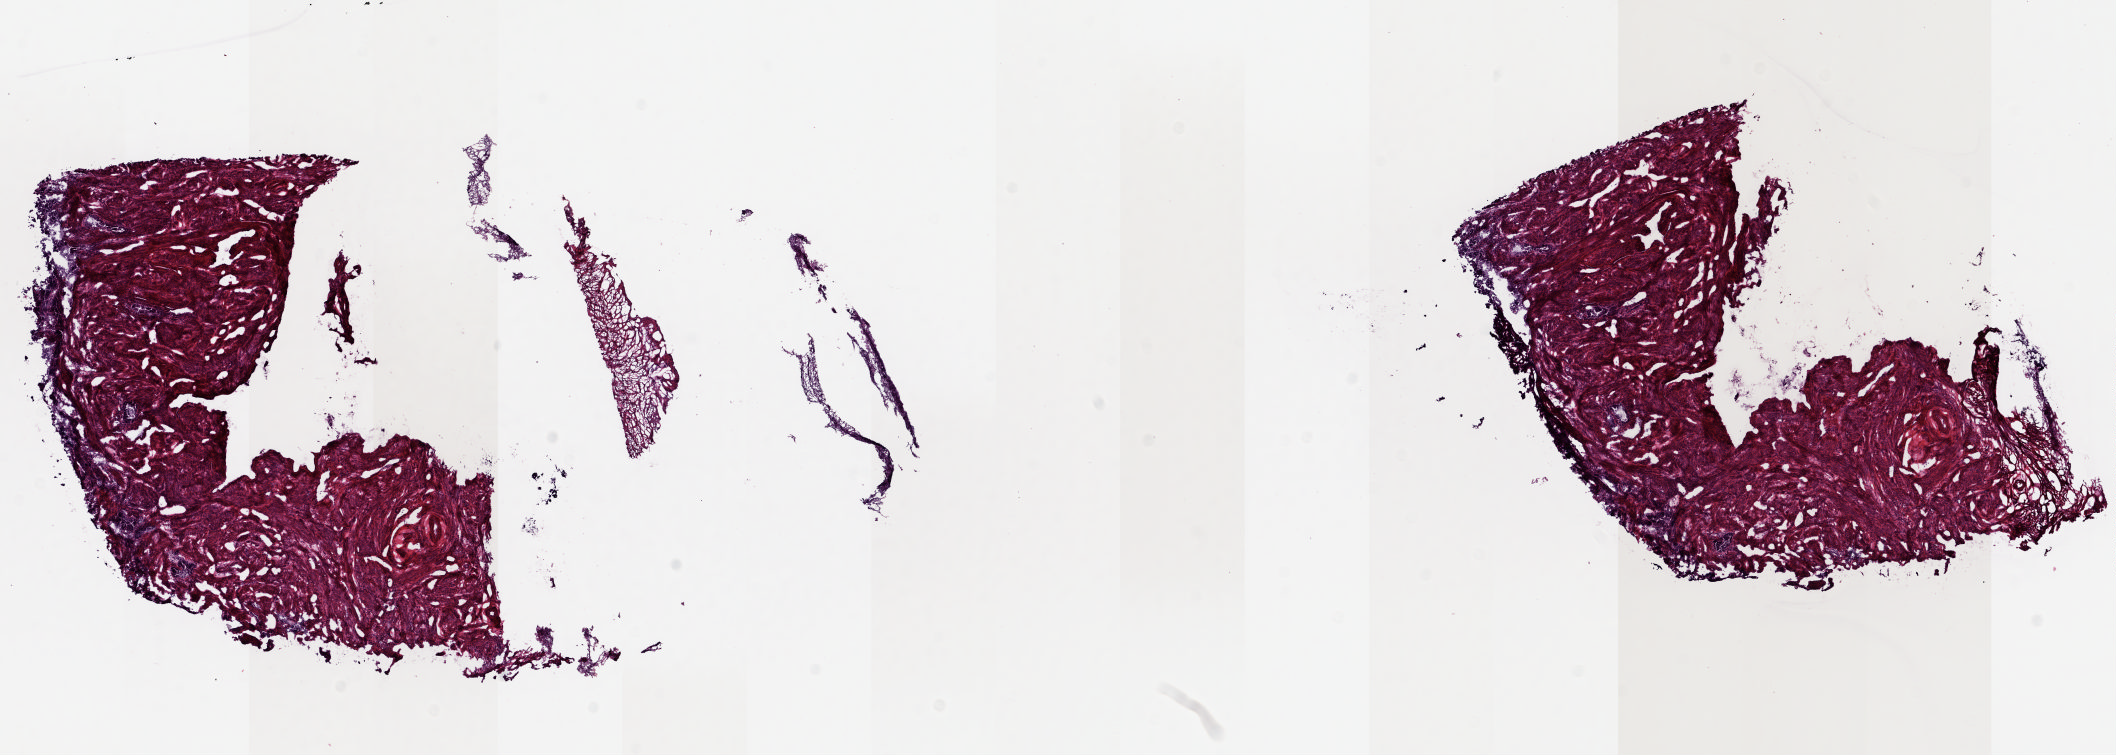
Digitized H&E tissue section (whole slide), shown as a low-resolution overview of the whole scanned area (about 16.8 x 6.0 mm). Frozen section from the top of the tissue portion. Sample: solid tissue normal (non-tumour tissue), uterus. Pathologist review of this section (percent, as recorded): tumour cells 0%, normal cells 100%.
This section: solid tissue normal sample (biorepository sample class).